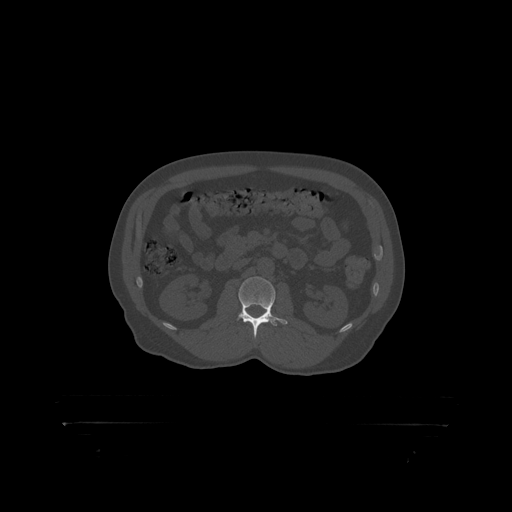
CT including the spine, one axial slice. 120 kVp. Bone window (W 1800 / L 400 HU). 1.25 mm slice thickness. 512 × 512 image matrix, field of view 650 × 650 mm. Male patient, age 46 years. From the clinical record (not read from this slice): primary cancer: skin.
Structures marked on this image (semi-automatic segmentation, software-assisted and operator-edited):
- L2 vertebra: box from (x=239, y=277) to (x=276, y=319) px